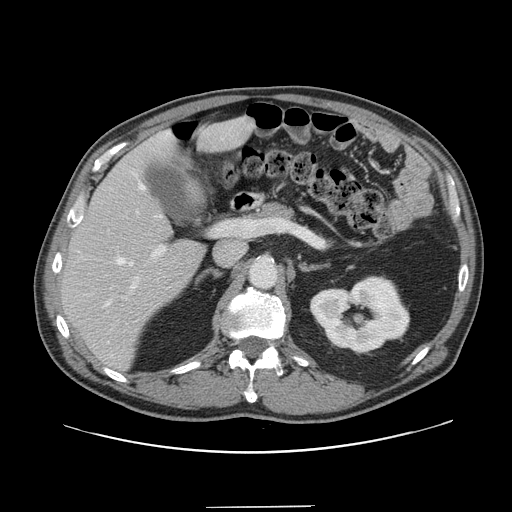
Contrast-enhanced abdominal CT, one axial slice. 120 kVp. Soft-tissue window (W 400 / L 40 HU). 2.5 mm slice thickness. 512 × 512 image matrix, field of view 397 × 397 mm. Male patient, age 64 years. From the clinical record (not read from this slice): diagnosis: colorectal cancer liver metastases, imaged before liver resection; multiple liver metastases: yes; largest metastasis: 3.5 cm; chemotherapy before resection: yes.
Structures marked on this image (outlined manually by an expert reader):
- hepatic veins: bounding box [x1, y1, x2, y2] px = [104, 172, 162, 307]
- liver: [62, 119, 251, 369]
- planned liver remnant (the part of the liver to remain after resection): [62, 119, 250, 368]
- portal vein (with intrahepatic branches): [131, 228, 218, 290]